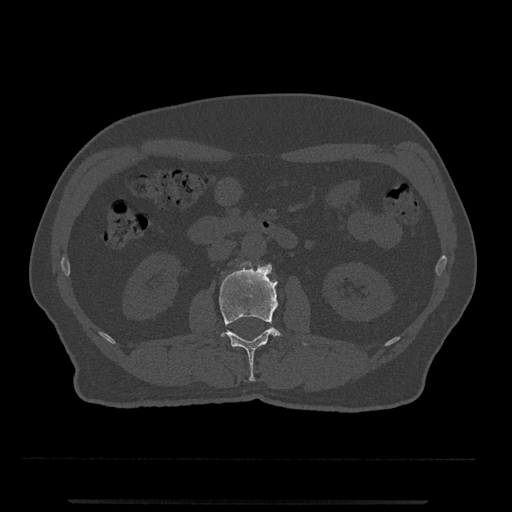
CT including the spine, one axial slice; slice 261 of 797 in the series (ordered by position); reconstruction kernel Br40s/3; 120 kVp; bone window (W 1800 / L 400 HU); 512 × 512 image matrix, field of view 419 × 419 mm. Patient: male, 63 years. Case-level facts recorded for this patient, not image findings: primary cancer: prostate.
Annotated regions visible in this slice (semi-automatic segmentation, software-assisted and operator-edited):
- L2 vertebra: bounding box [x1, y1, x2, y2] px = [219, 262, 307, 382]